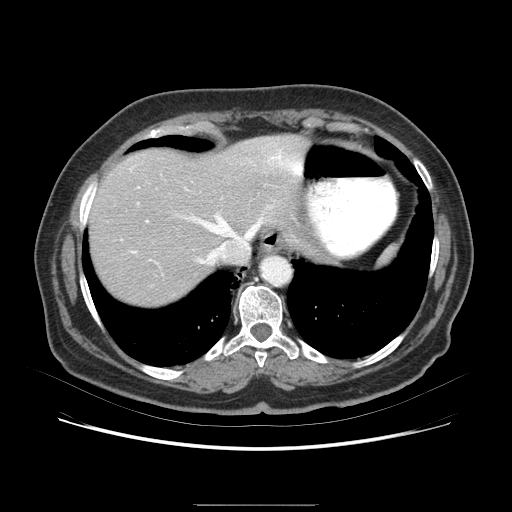
Contrast-enhanced abdominal CT (liver protocol), one axial slice; slice 66 of 79 in the series (ordered by position); 120 kVp; soft-tissue window (W 400 / L 40 HU); 2.5 mm slice thickness; 512 × 512 image matrix, field of view 380 × 380 mm. From the clinical record (not read from this slice): diagnosis: hepatocellular carcinoma (patient treated with transarterial chemoembolisation; whether this scan precedes or follows treatment is not stated here); TNM stage (as recorded): Stage-I; Child-Pugh class: A; tumour differentiation: poorly differentiated; tumour nodularity: uninodular.
Annotated regions visible in this slice (semi-automatic segmentation, software-assisted and operator-edited):
- liver parenchyma outside the tumour (the mass and vessels are separate outlines, so this box may not span the whole liver): box from (x=94, y=142) to (x=326, y=284) px
- liver vessels: (x=147, y=174)–(x=320, y=229)